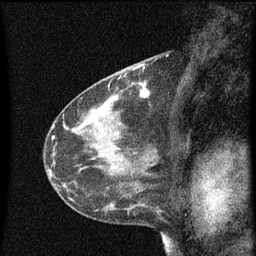
Breast MRI (dynamic contrast-enhanced), one sagittal slice; position 30 of 60 along the scan axis; dynamic contrast-enhanced series, image 2 of 3 at this slice position (ordered by acquisition); 1.5 T; TE 4.2 ms, TR 8 ms; 256 × 256 image matrix. Female patient, age 41 years.
Outlined on this slice (semi-automatically segmented with operator editing):
- analysis volume of interest (the breast-tissue region the enhancement analysis was run in; not a lesion): bounding box <130,76,157,101> (left, top, right, bottom; pixels)
- tumour enhancement mask (voxels above the 70 % enhancement threshold inside the analysis volume of interest): <138,82,151,99>